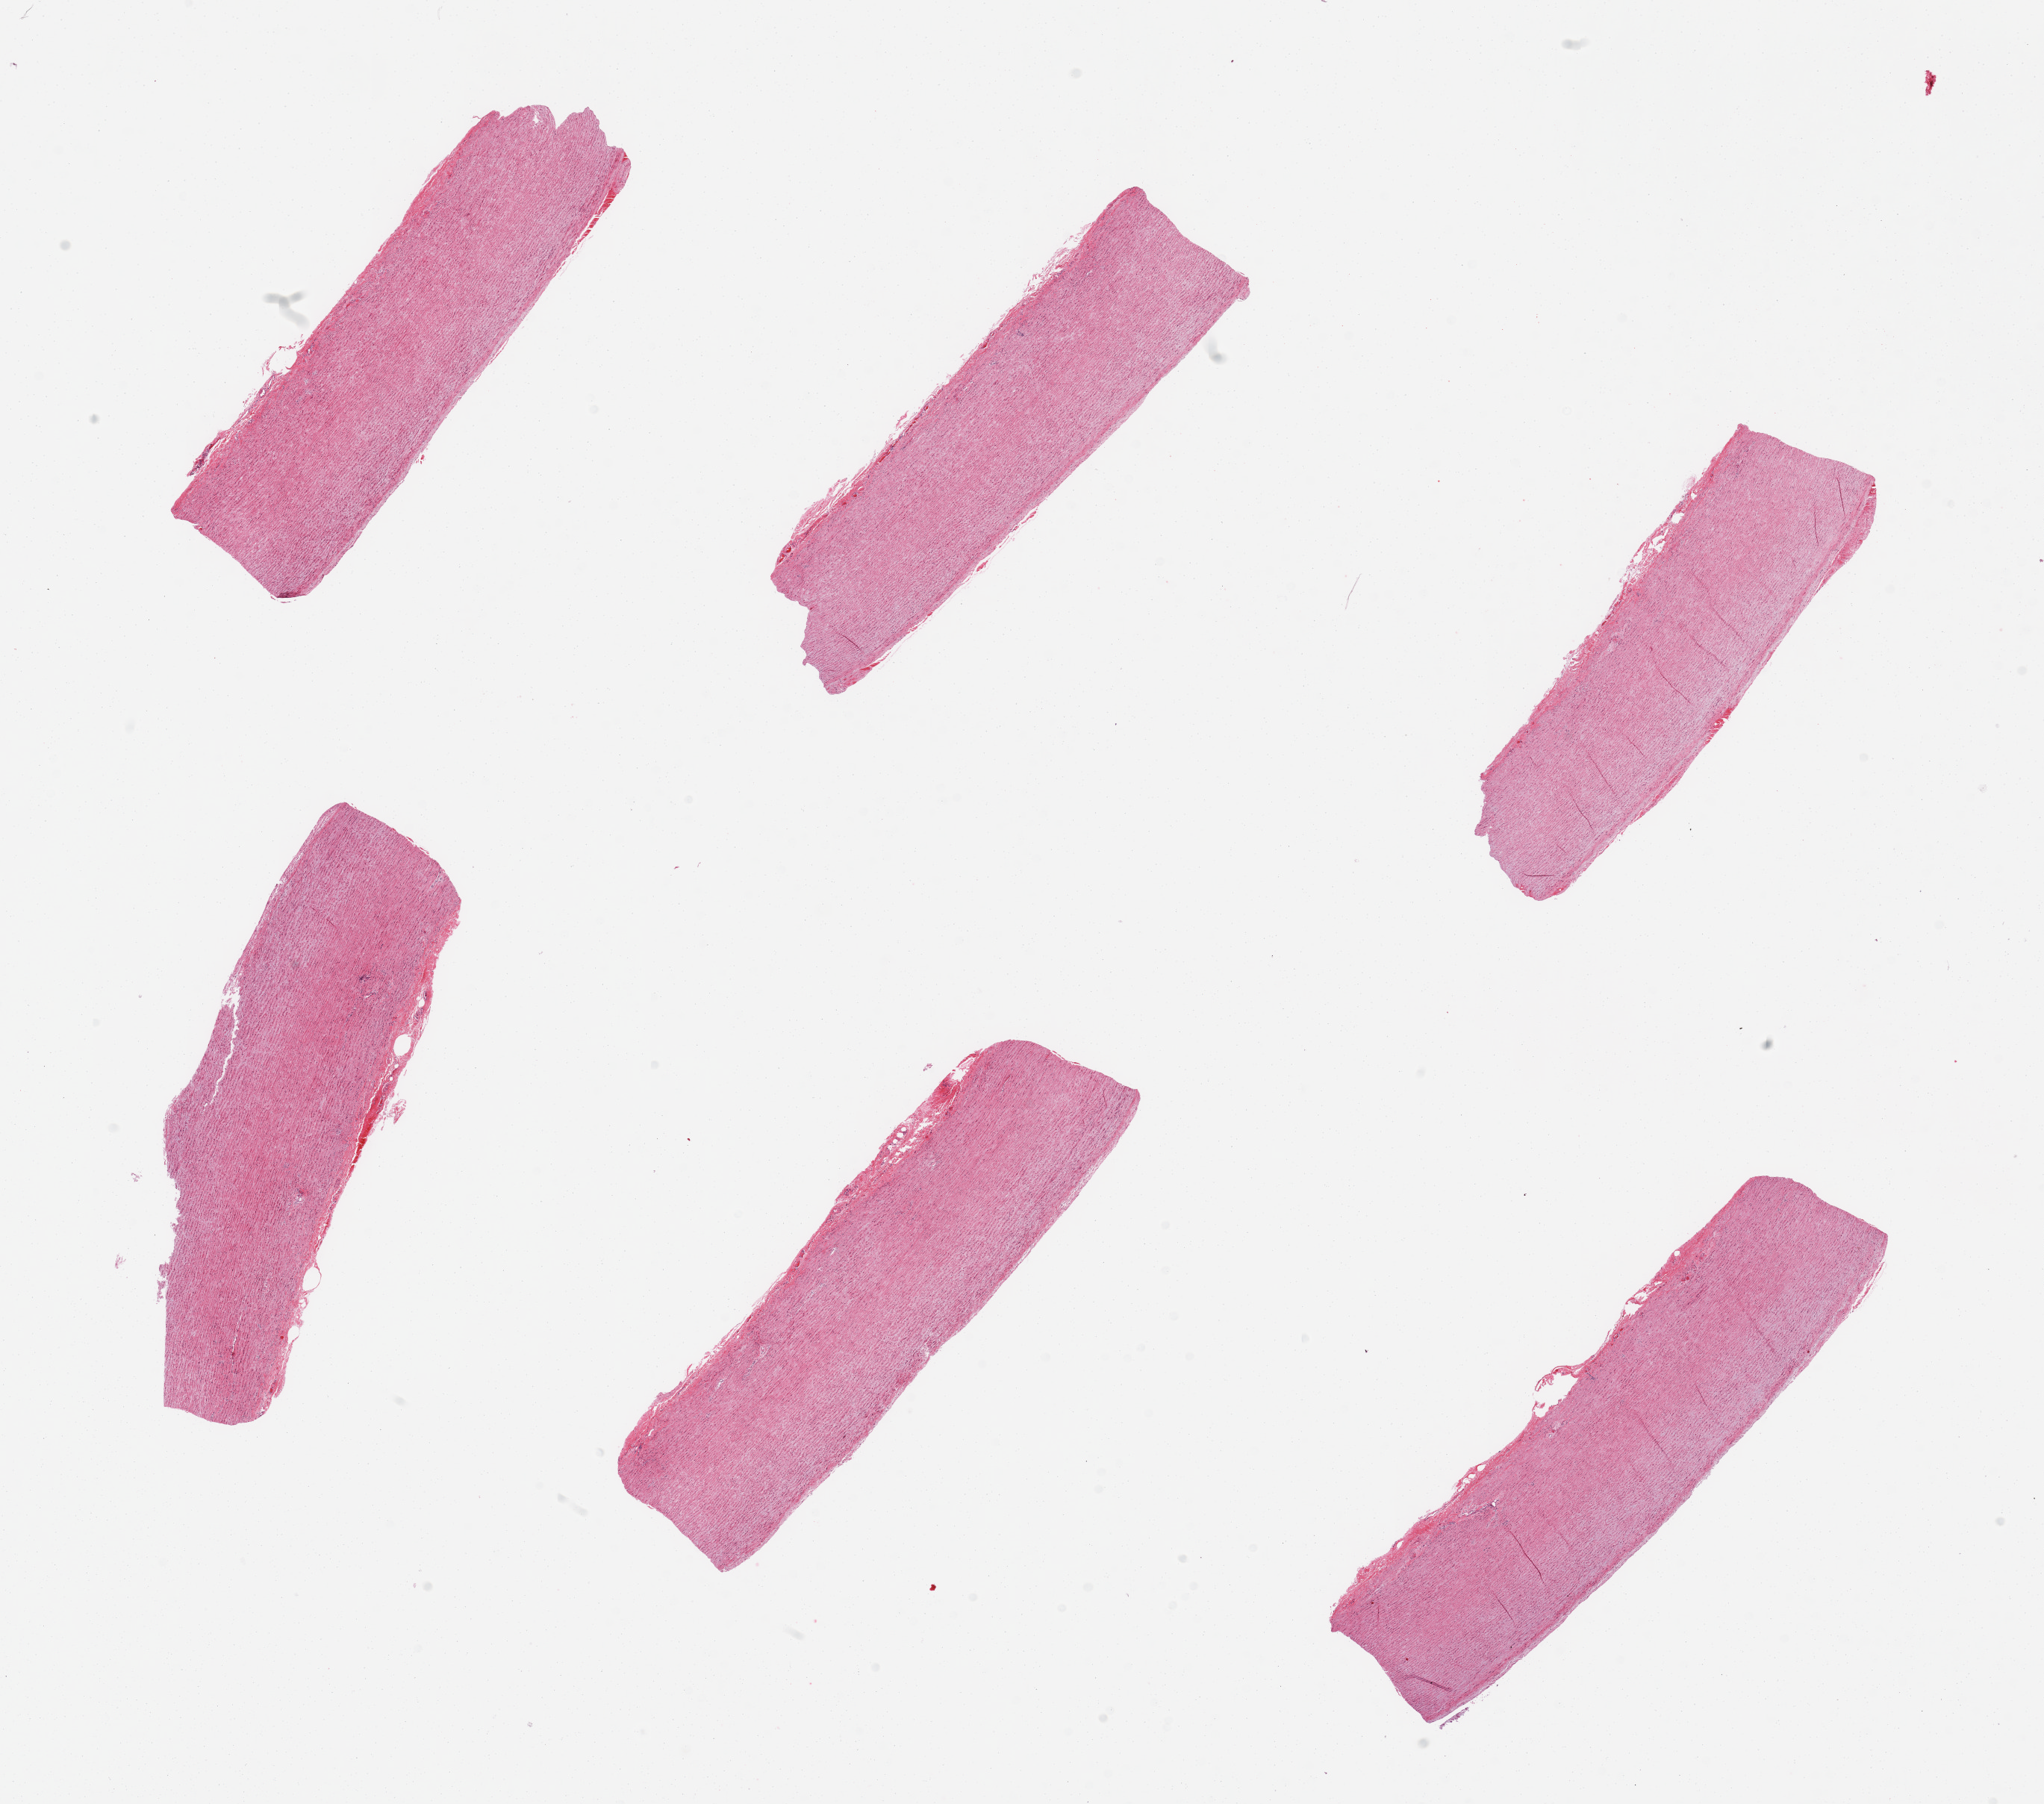
Digitized haematoxylin and eosin-stained section, brightfield, a low-resolution overview of the entire scanned area, about 21.7 x 19.1 mm (slide scanned at 20x), PAXgene-fixed paraffin-embedded (PFPE) section, sampled site (target tissue): aorta, donor tissue sample. Female donor.
Review note (as recorded): 6 pieces.